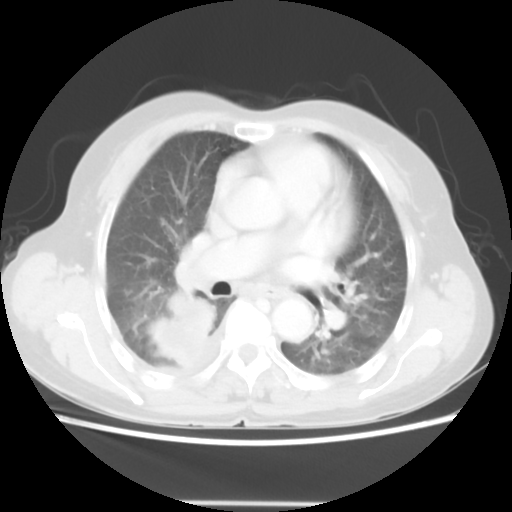
Chest CT, one axial slice; reconstruction kernel STANDARD; 140 kVp; lung window (W 1500 / L -600 HU); 512 × 512 image matrix. Female patient, age 67 years. From the clinical record (not read from this slice): clinical TNM (as recorded): T3 N1 M1.
Annotated regions visible in this slice (bounding box drawn by a radiologist):
- lung tumour (recorded histology: adenocarcinoma): bounding box (x1, y1, x2, y2) in pixels: (149, 286, 217, 365)